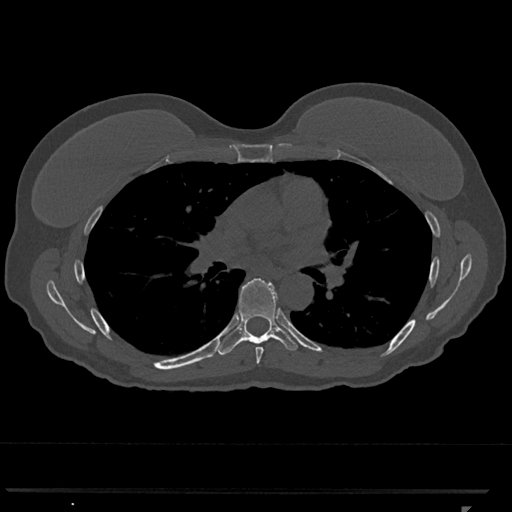
CT including the spine, one axial slice; position 729 of 793 along the scan axis; reconstruction kernel Br40s/3; bone window (W 1800 / L 400 HU); 512 × 512 image matrix, field of view 380 × 380 mm. Female patient, age 62 years. From the clinical record (not read from this slice): primary cancer: renal.
Outlined on this slice (semi-automatic segmentation, software-assisted and operator-edited):
- T6 vertebra: bounding box (x1, y1, x2, y2) in pixels: (255, 343, 264, 364)
- T7 vertebra: (216, 278, 298, 355)